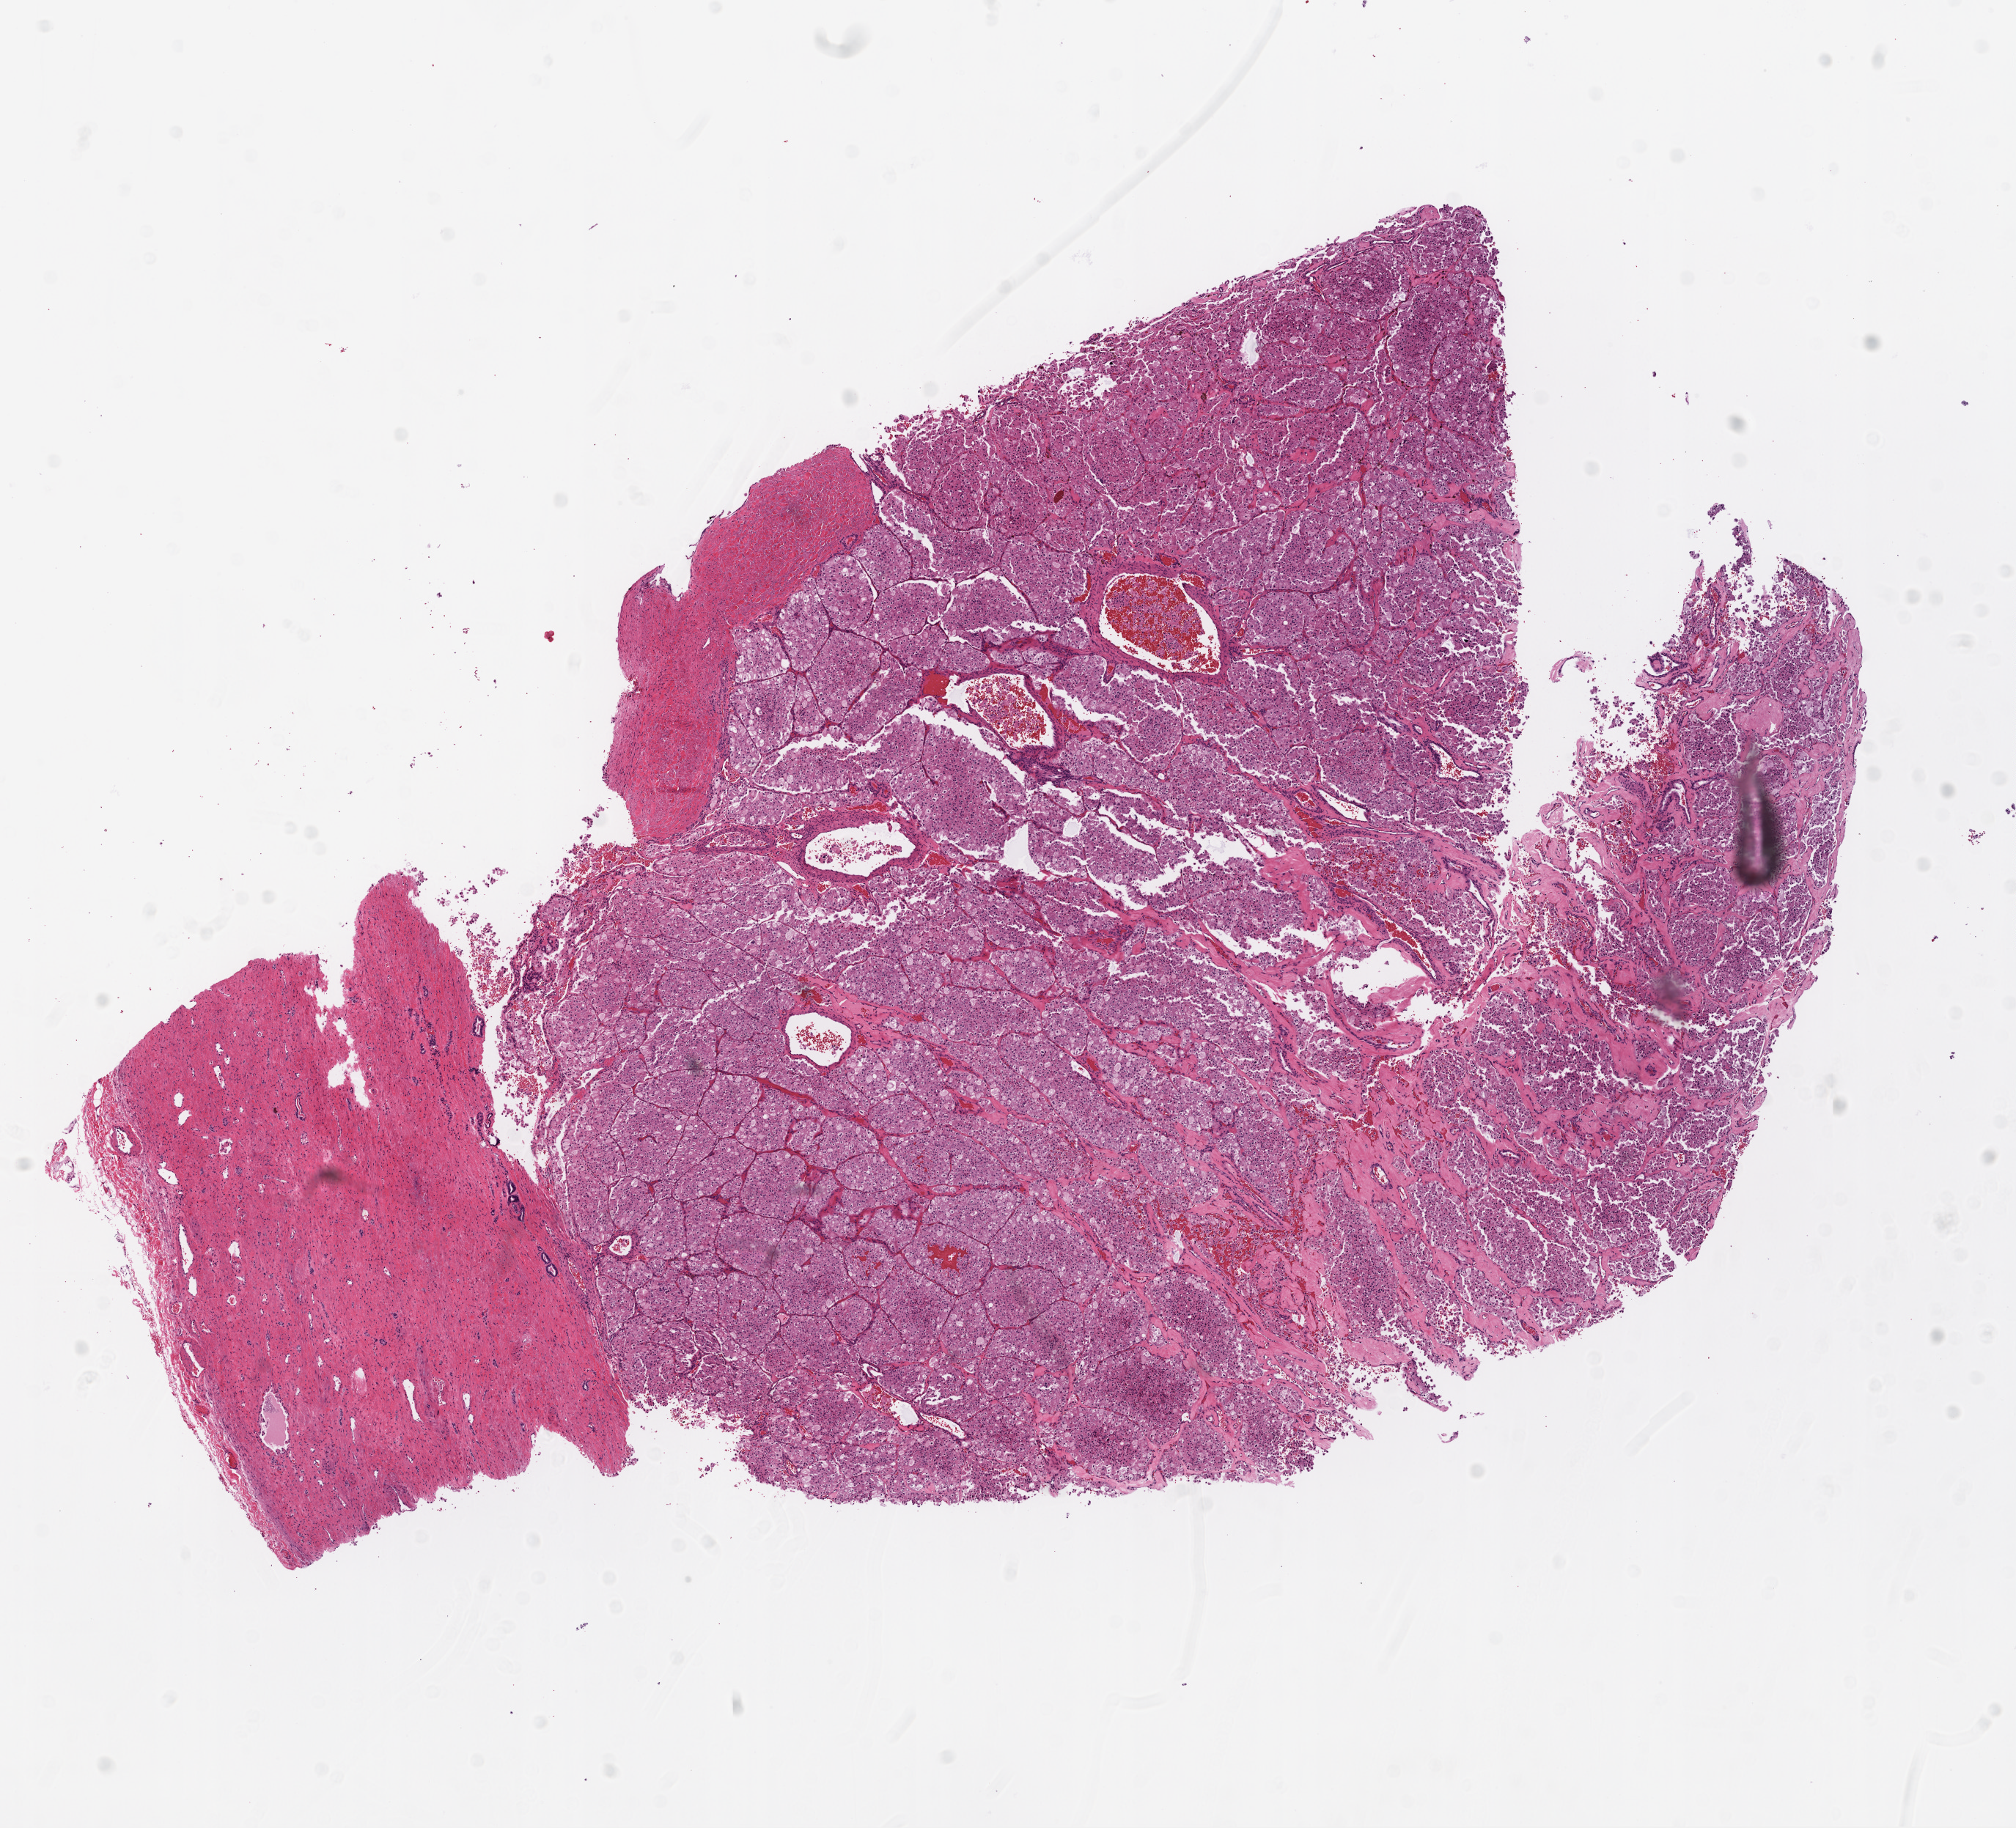
Whole-slide histology image, Hematoxylin and eosin (H&E) stained — shown as a low-resolution overview of the whole scanned area (about 11.0 x 10.0 mm, acquisition: 20x scan); frozen section from the top of the tissue portion; primary tumour sample from the kidney. Patient: male, age at initial diagnosis 59 years. Histologic grade: G2 (moderately differentiated). Slide review estimates, as recorded: tumour cells 83%, tumour nuclei 90%, normal cells 15%, stromal cells 2%, necrosis 0%.
Laterality: right. Diagnosis: Clear cell adenocarcinoma, NOS. AJCC pathologic stage: II.